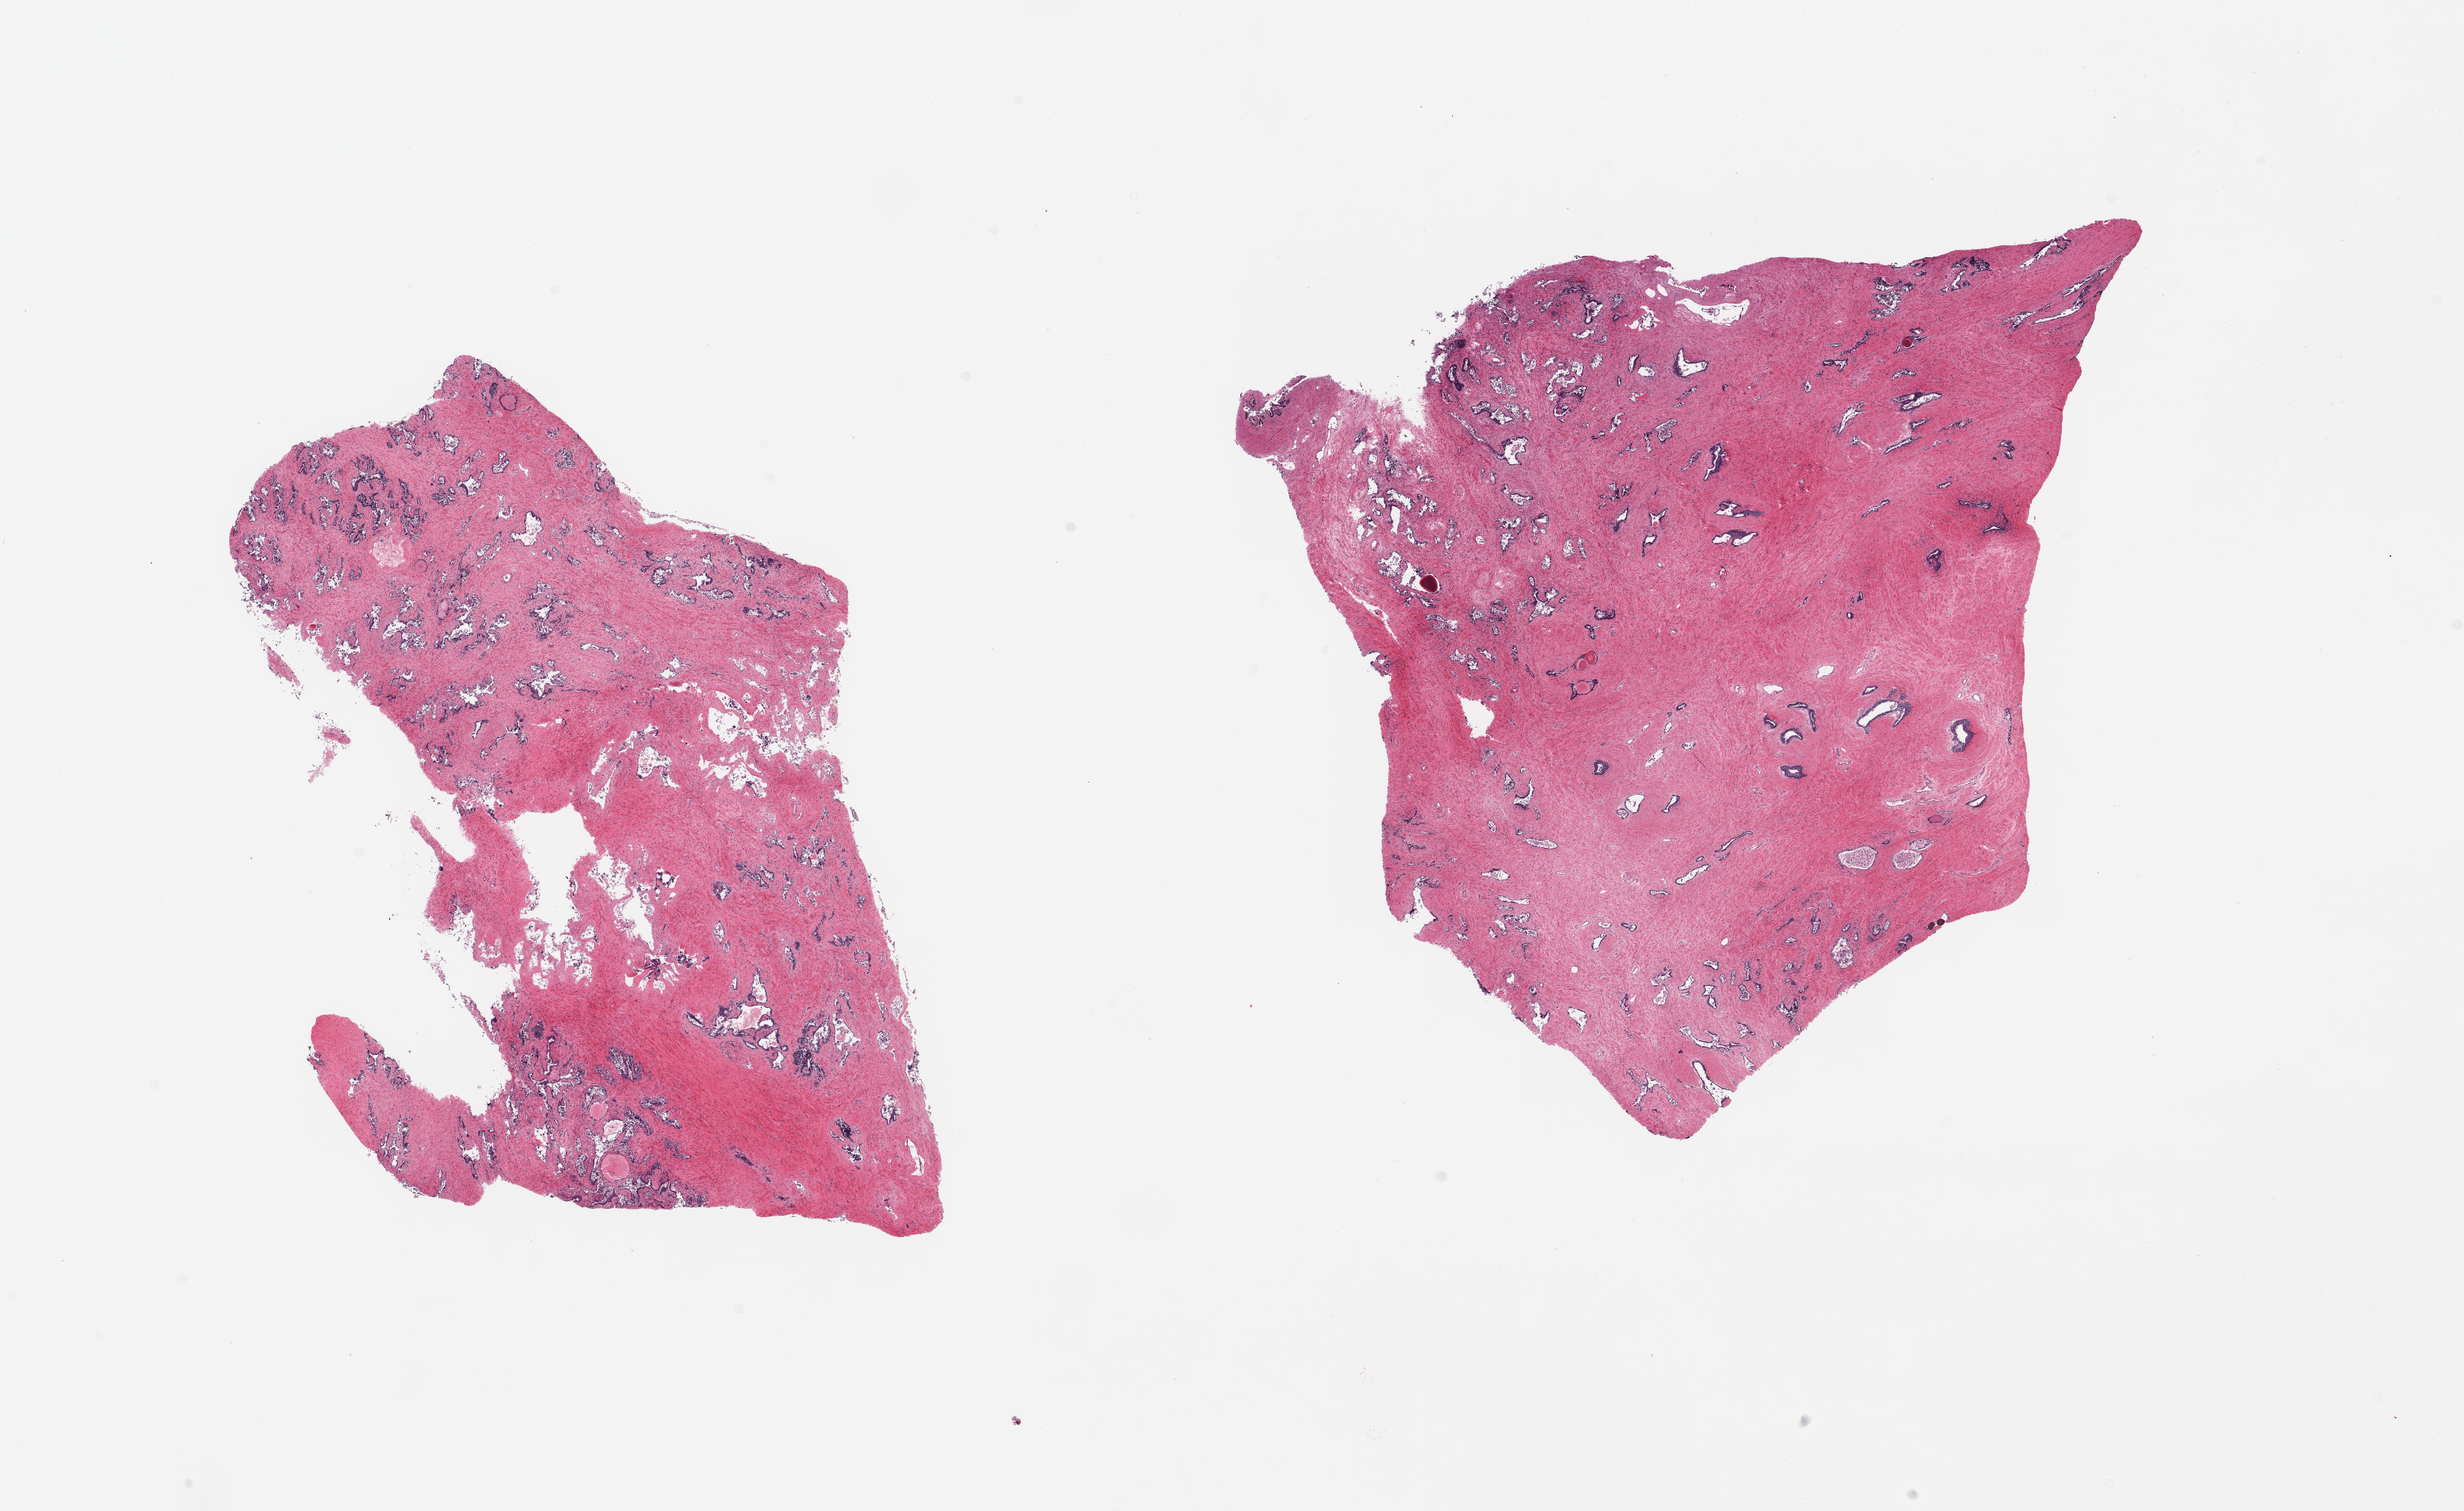
Digitized haematoxylin and eosin-stained section, a low-resolution overview of the entire scanned area, about 25.6 x 15.7 mm (slide scanned at 20x). PAXgene-fixed paraffin-embedded (PFPE) section. Section of prostate (target tissue). Tissue donor sample. Male donor.
* pathologist's review note for this sample: 2 pieces; sloughing of glandular epithelium, transitional metaplasia, focus of seminal vesicle